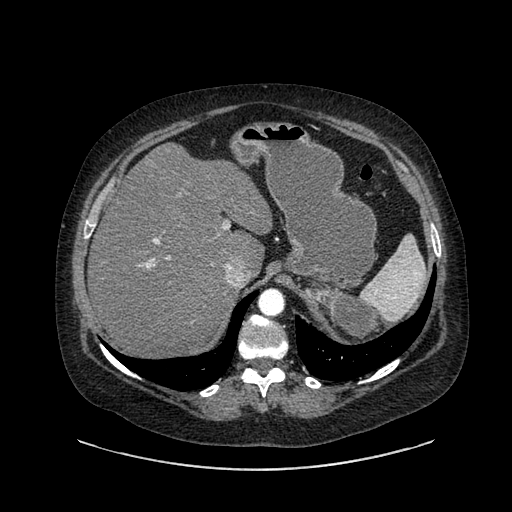
Contrast-enhanced abdominal CT, one axial slice. Position 634 of 769 along the scan axis. Reconstruction kernel SOFT. 120 kVp. Intravenous contrast given. Soft-tissue window (W 400 / L 40 HU). 512 × 512 image matrix. Female patient, age 61 years. Case-level facts recorded for this patient, not image findings: diagnosis: adrenocortical carcinoma; tumour side: left adrenal; tumour size at pathology: 13 cm; Ki-67 index: 79 %; stage (as recorded): 2.
Structures marked on this image (semi-automatically segmented with operator editing):
- mass: bounding box <309,281,376,342> (left, top, right, bottom; pixels)